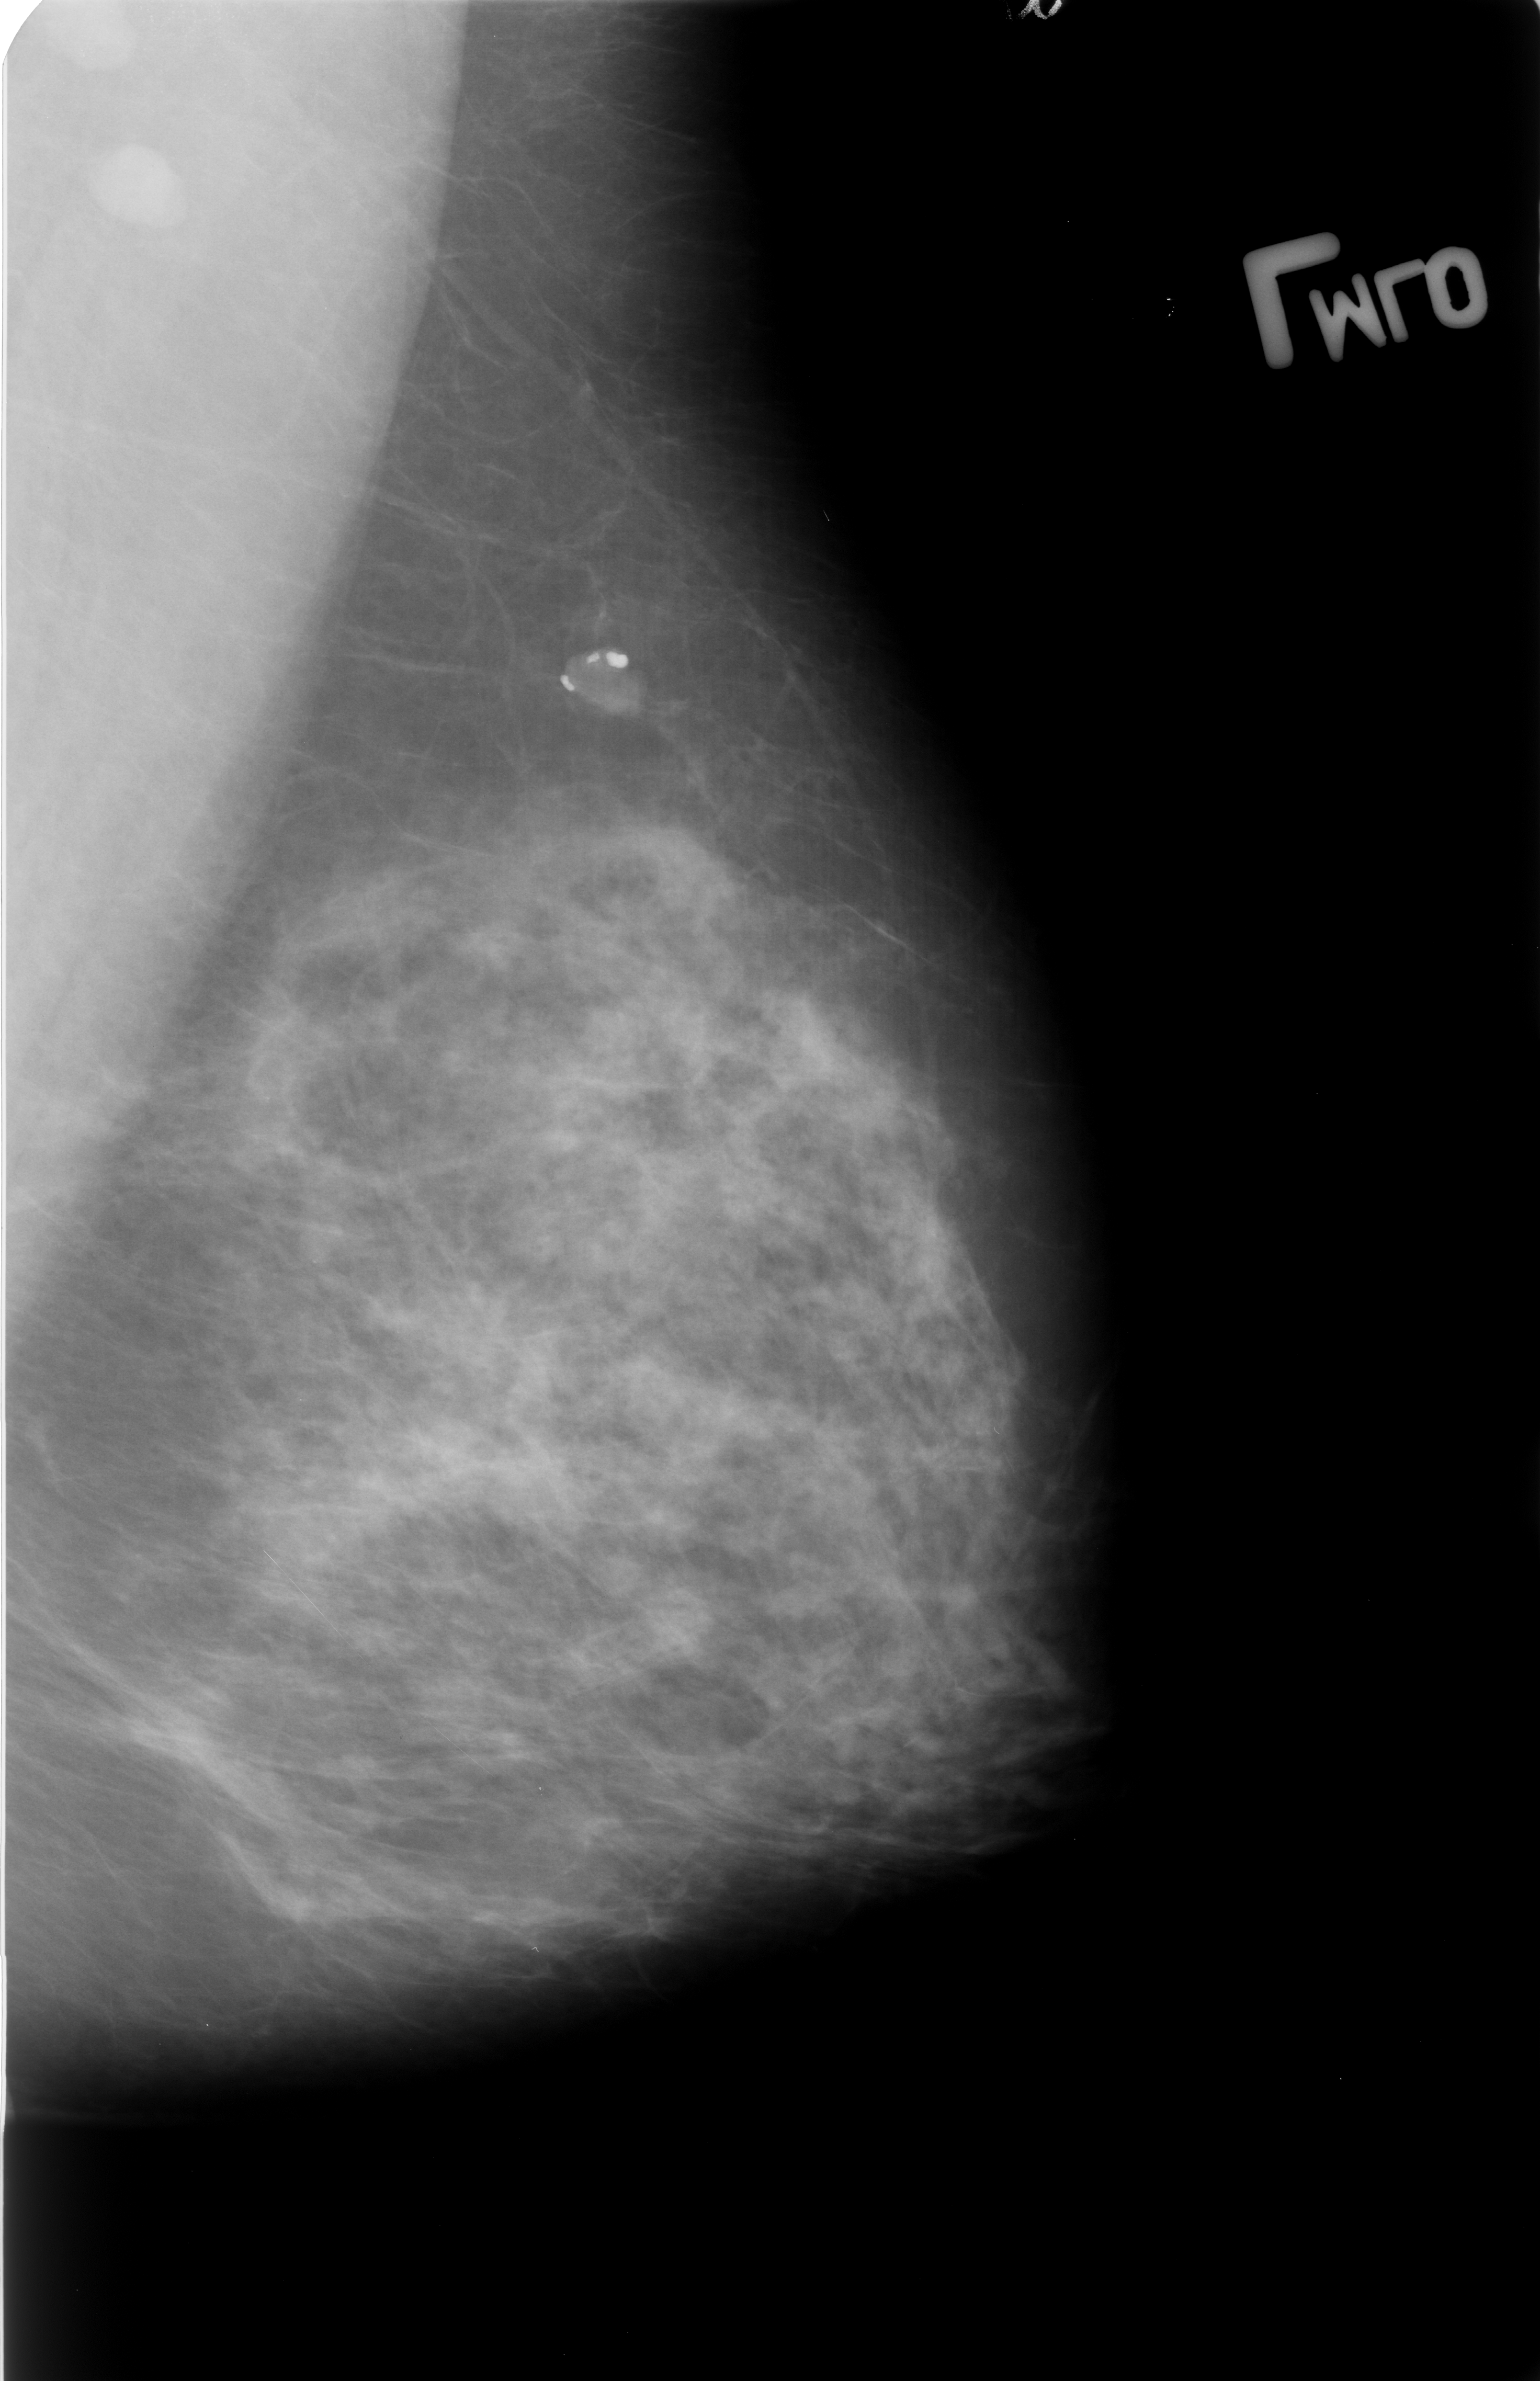
Digitized screen-film mammogram; left breast; mediolateral oblique (MLO) view; BI-RADS breast density category 3 (scale 1–4); 1540 × 2381 image matrix.
Expert-marked regions of interest on this film, with their recorded descriptors:
- calcifications, morphology coarse; BI-RADS assessment category 2; subtlety rating 3 on a 1 (subtle) to 5 (obvious) scale; outcome (as recorded, no biopsy): benign without callback (not worked up further): bounding box <552,644,658,725> (left, top, right, bottom; pixels)